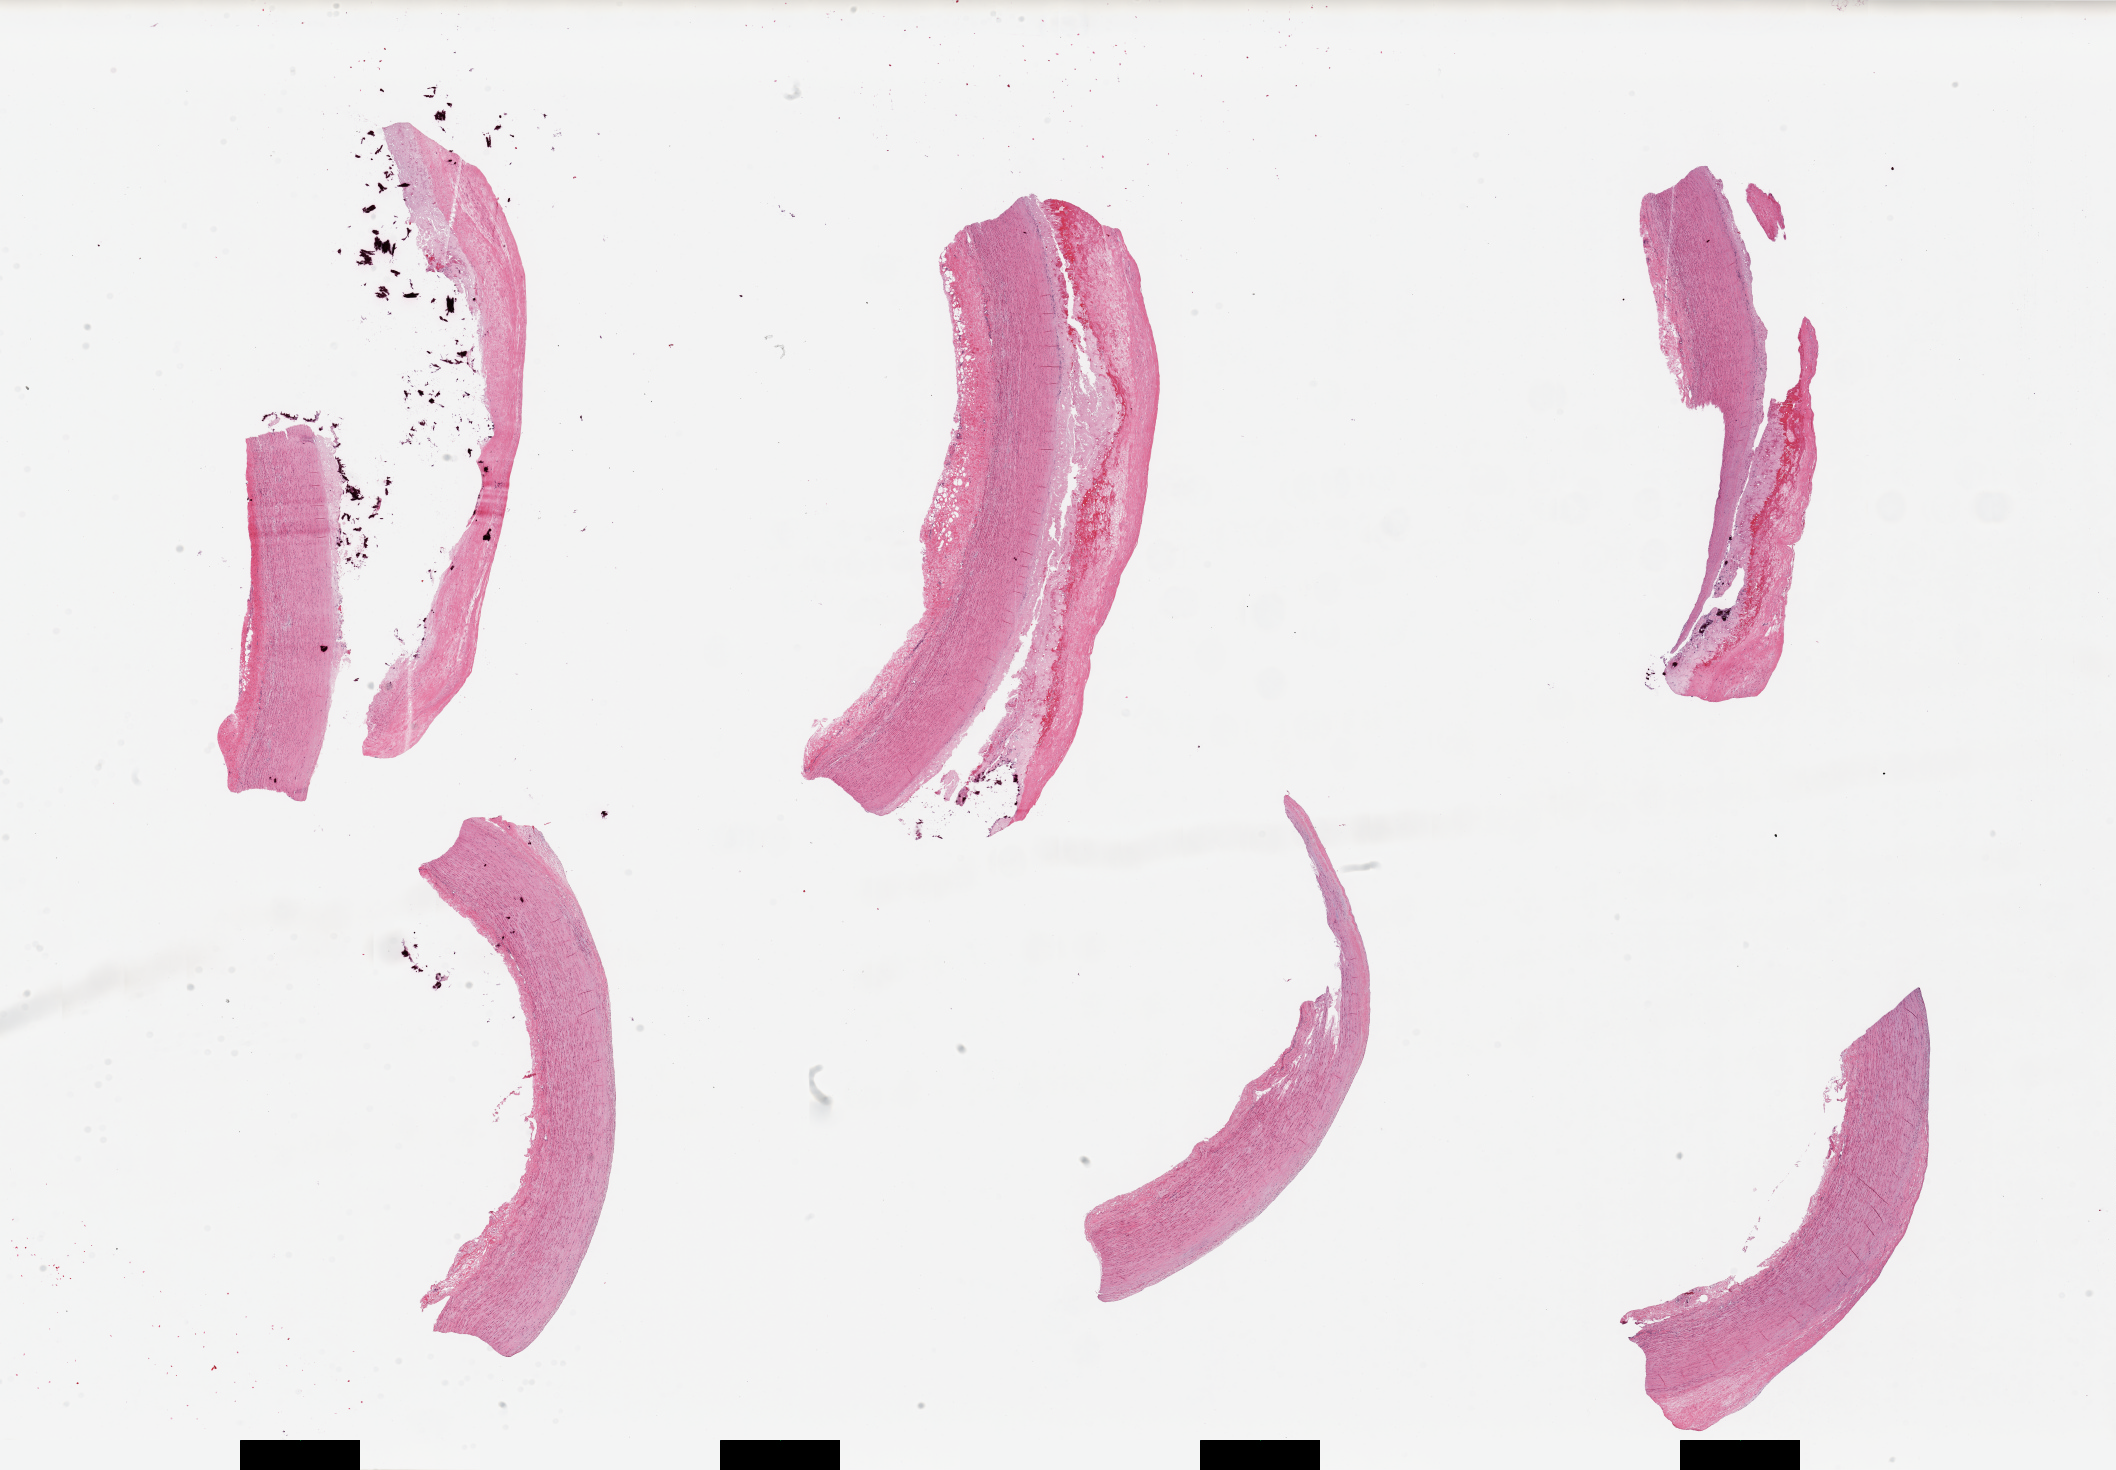
Whole-slide image, hematoxylin and eosin (H&E) stain — low-resolution overview of the scanned area, about 33.5 x 23.3 mm (acquisition: 20x scan), PAXgene-fixed, paraffin-embedded tissue, sampled site (target tissue): aorta, tissue donor sample. Donor sex: male.
Reviewer comment on this tissue sample: 6 pieces, up to 11x5mm; Prominent sclerotic plaques in 3/6.